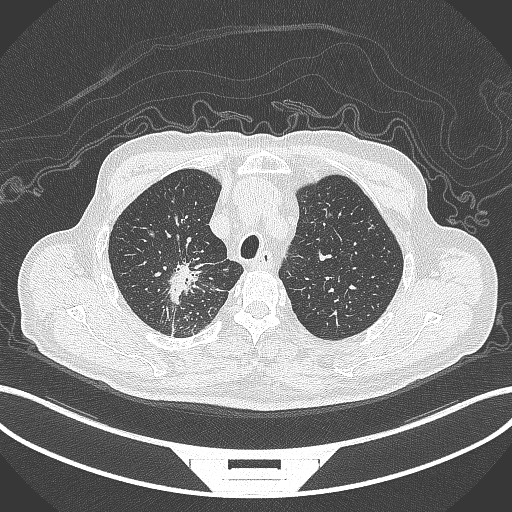
Chest CT, one axial slice; slice 304 of 407 in the series (ordered by position); 120 kVp; lung window (W 1500 / L -600 HU); 1 mm slice thickness; 512 × 512 image matrix, field of view 400 × 400 mm. Patient: male, 69 years. From the clinical record (not read from this slice): clinical TNM (as recorded): T1c N1 M1.
Structures marked on this image (bounding box drawn by a radiologist):
- lung tumour (recorded histology: adenocarcinoma): box from (x=162, y=259) to (x=206, y=307) px